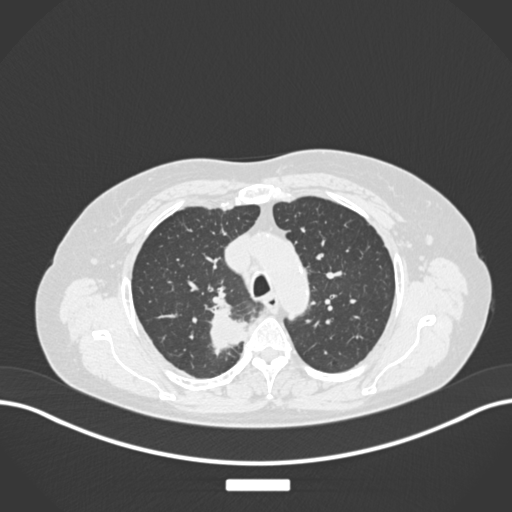
Chest CT, one axial slice; position 191 of 237 along the scan axis; lung window (W 1500 / L -600 HU); 512 × 512 image matrix, field of view 400 × 400 mm. Female patient, age 62 years. Case-level facts recorded for this patient, not image findings: clinical TNM (as recorded): T1c N1 M0.
Annotated regions visible in this slice (rectangle marked by the reading radiologist):
- lung tumour (recorded histology: squamous cell carcinoma): box from (x=208, y=309) to (x=249, y=354) px